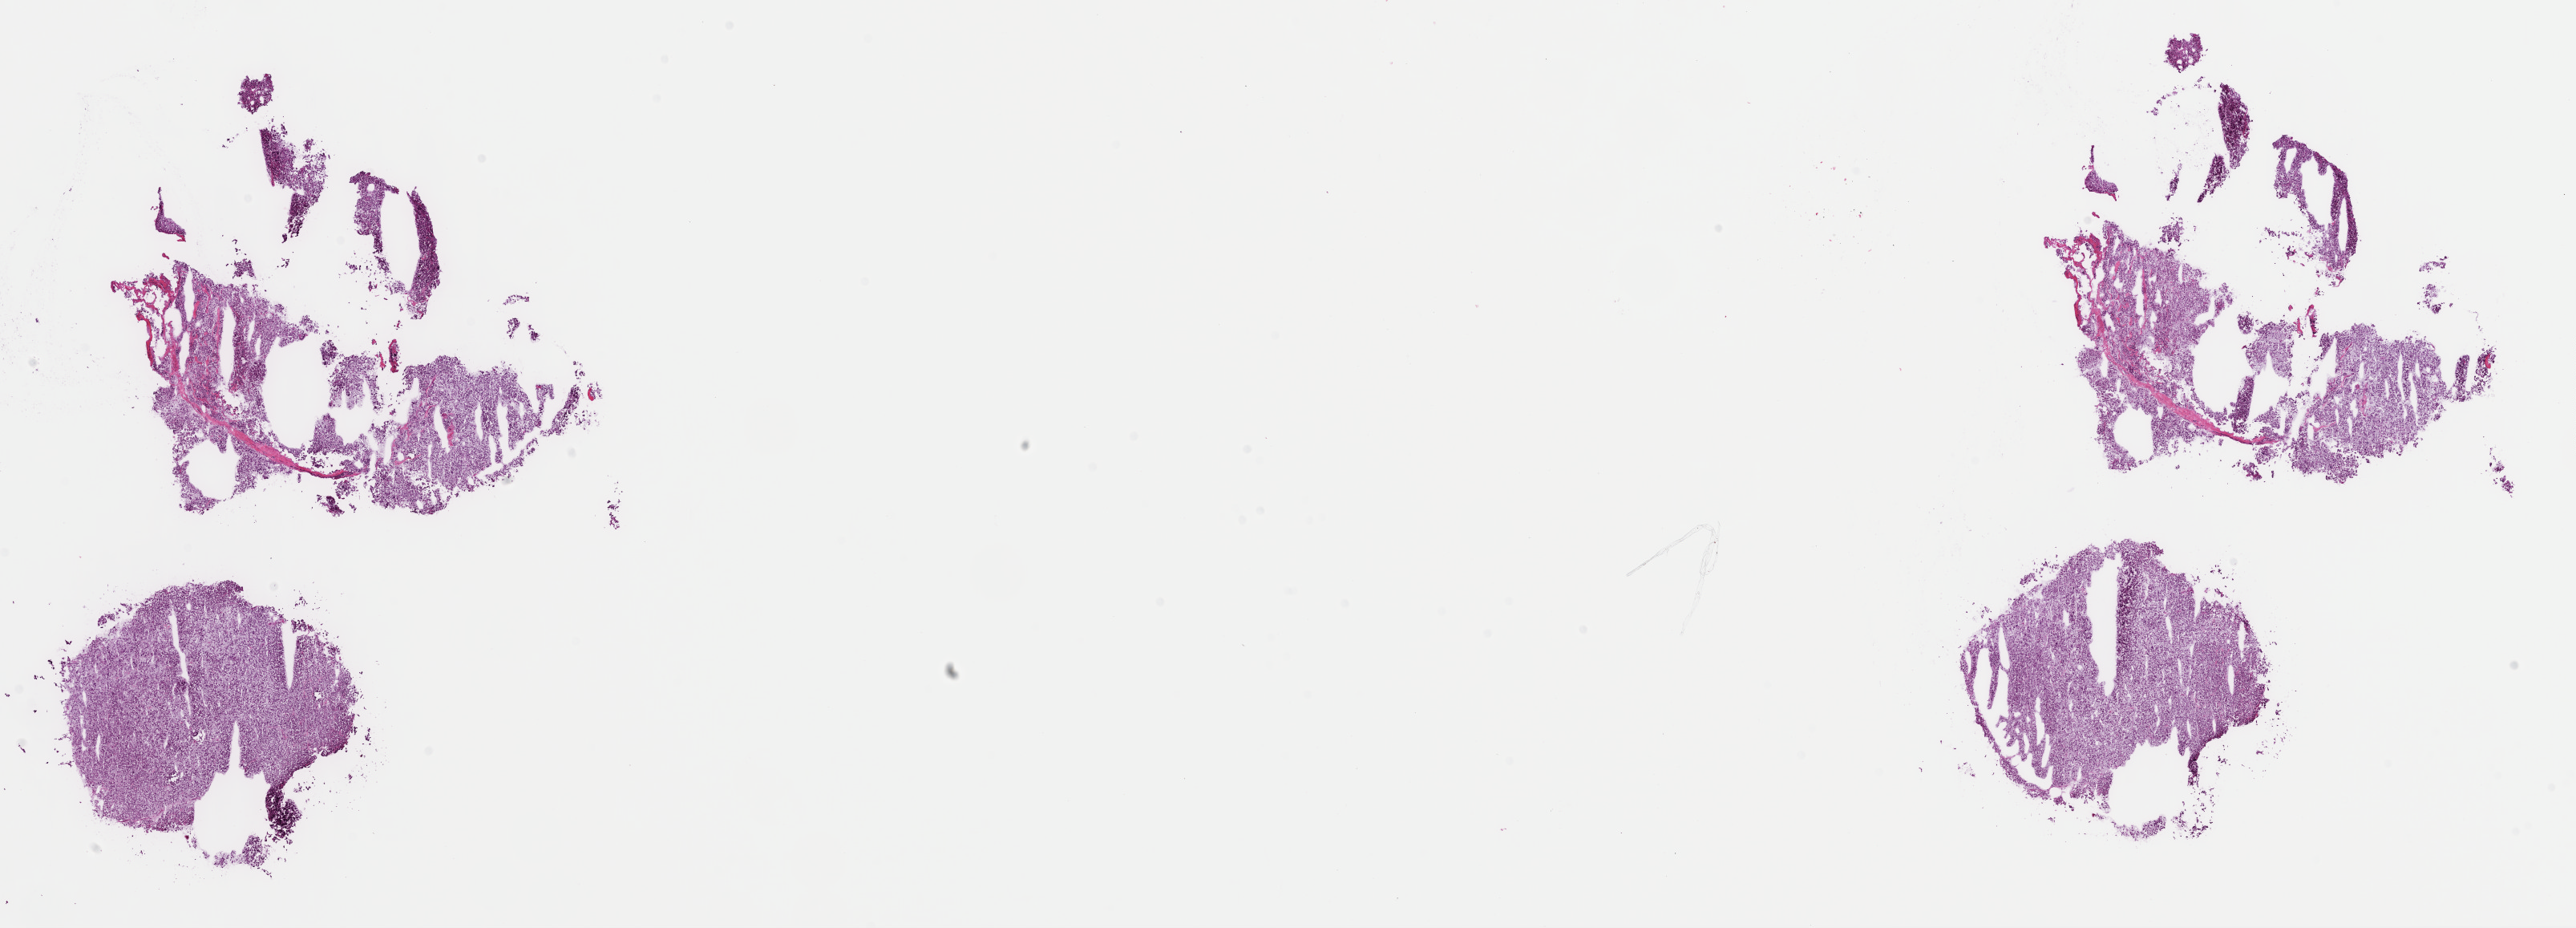
H&E-stained whole-slide image — a low-resolution overview of the entire scanned area, about 25.4 x 9.1 mm (slide scanned at 40x). Frozen section from the top of the tissue portion. Sample: primary tumour, adrenal gland. Female, age 46 years at initial diagnosis.
Pathologic diagnosis: Pheochromocytoma, NOS.